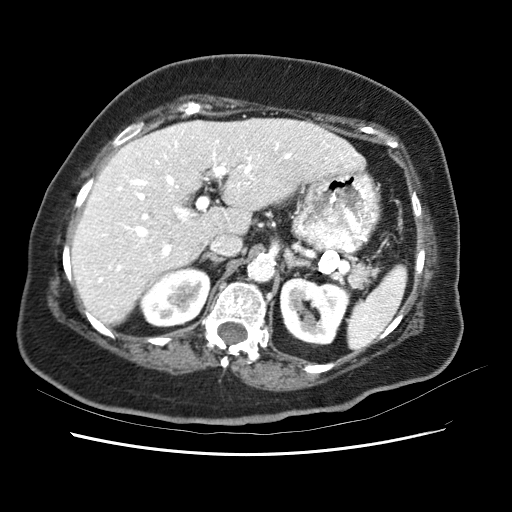
Contrast-enhanced abdominal CT (liver protocol), one axial slice; slice 38 of 62 in the series (ordered by position); 120 kVp; soft-tissue window (W 400 / L 40 HU); 2.5 mm slice thickness; 512 × 512 image matrix, field of view 340 × 340 mm. Case-level facts recorded for this patient, not image findings: diagnosis: hepatocellular carcinoma (patient treated with transarterial chemoembolisation; whether this scan precedes or follows treatment is not stated here); TNM stage (as recorded): Stage-I; Child-Pugh class: B.
Annotated regions visible in this slice (semi-automatic segmentation, software-assisted and operator-edited):
- liver parenchyma outside the tumour (the mass and vessels are separate outlines, so this box may not span the whole liver): bounding box [x1, y1, x2, y2] px = [72, 116, 366, 326]
- mass: [264, 150, 314, 209]
- liver vessels: [81, 128, 355, 310]